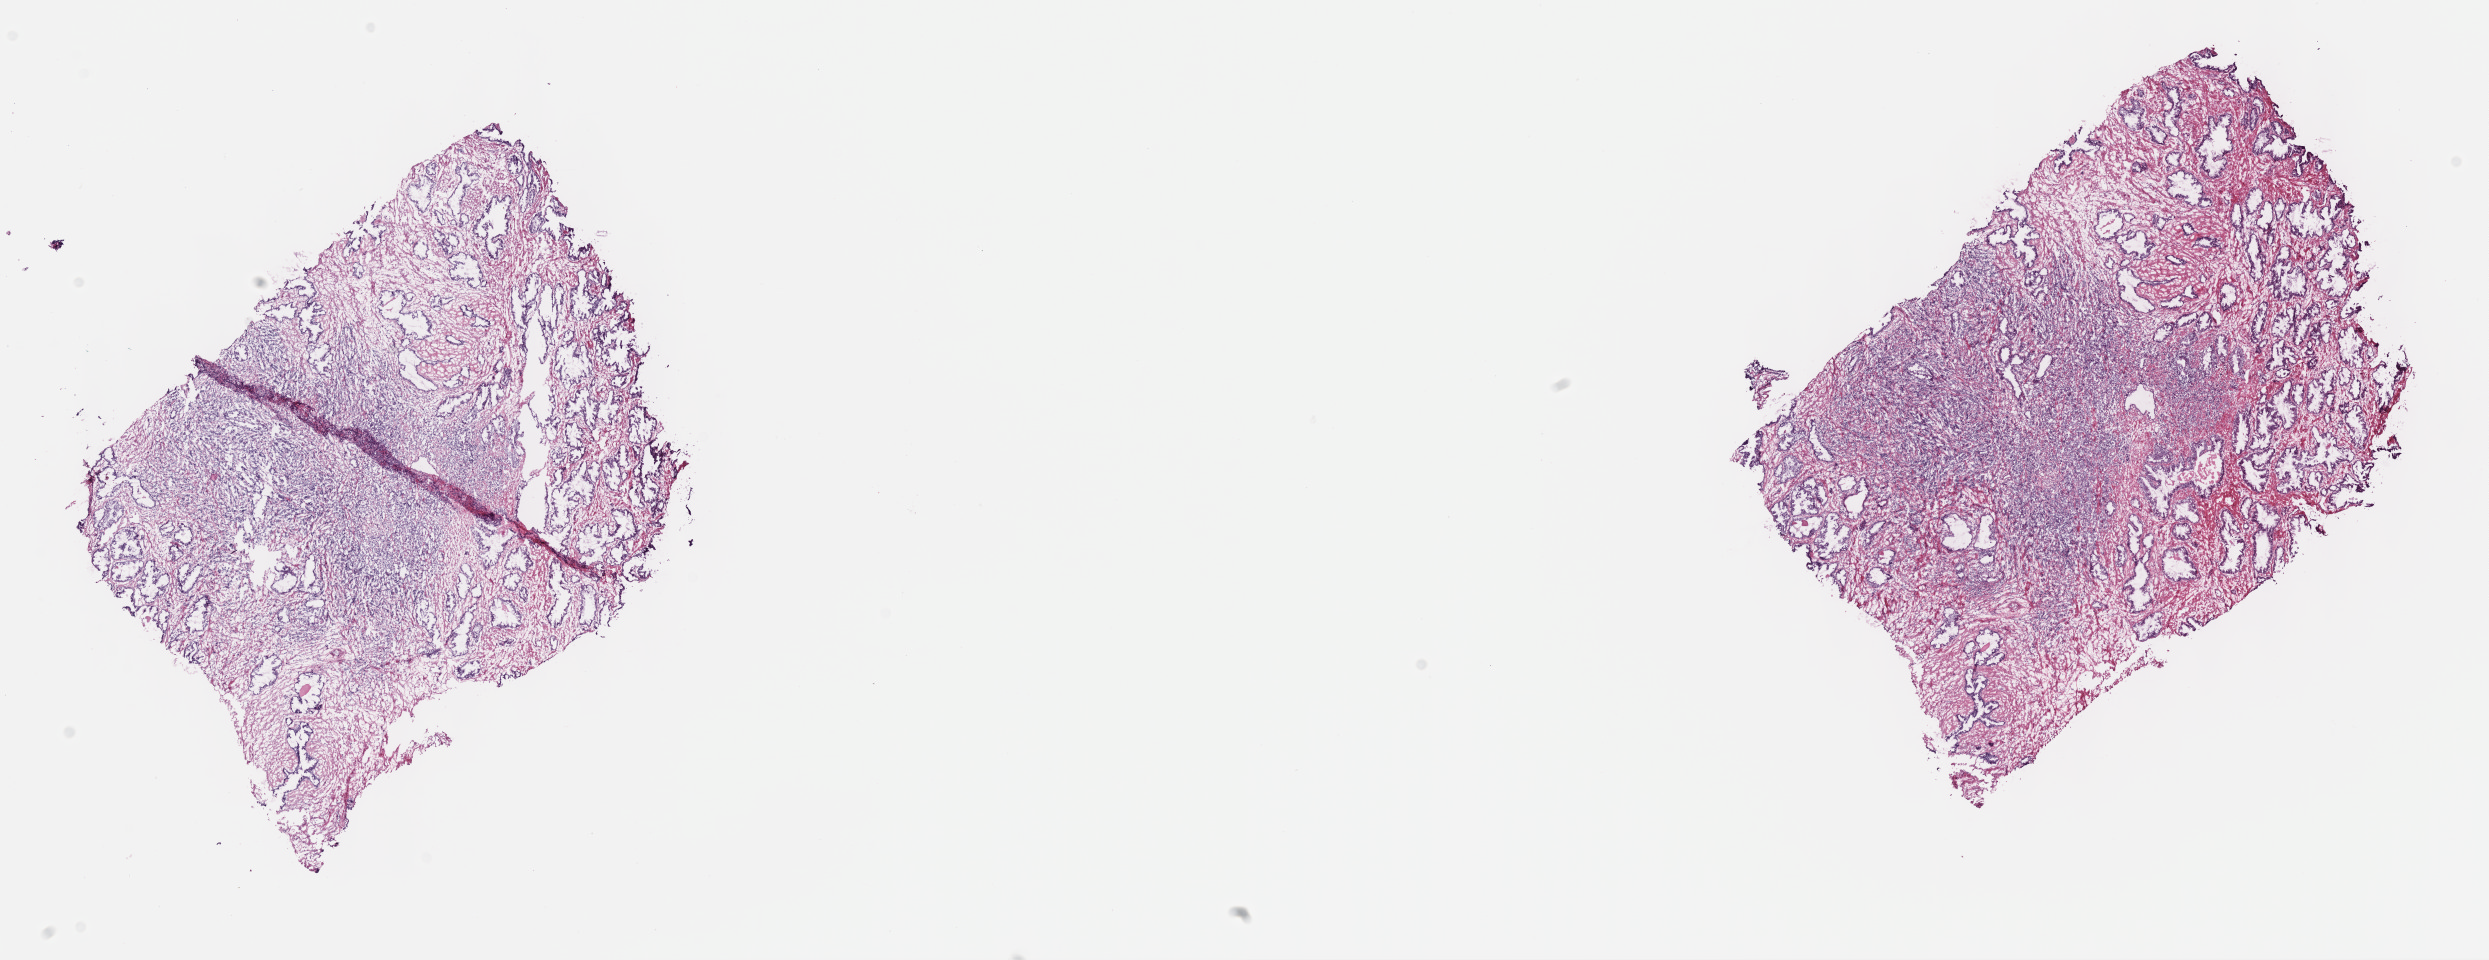
Whole-slide histology image, H&E-stained — a low-resolution overview of the entire scanned area, about 20.1 x 7.8 mm. Frozen section from the top of the tissue portion. Prostate, primary tumour sample. Male patient; age at initial diagnosis 59 years. Gleason score: 8 (4+4). Pathologist review of this section (percent, as recorded): tumour cells 43%, tumour nuclei 60%, normal cells 20%, stromal cells 35%, necrosis 2%. Inflammatory infiltration, as recorded: lymphocyte infiltration 20%, monocyte infiltration 0%, neutrophil infiltration 0%.
Lymph nodes positive (case pathology): 0 of 16 examined. Histologic diagnosis: Adenocarcinoma, NOS (prostate gland).